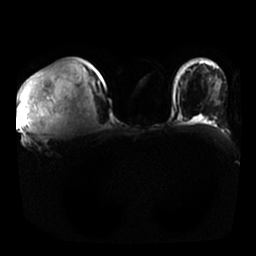
Breast MRI, one axial slice; diffusion-weighted series; image 2 of 4 stored at this slice position (different b-values; order by instance number); 1.5 T; 256 × 256 image matrix. Female patient.
Annotated regions visible in this slice (manually delineated by an expert):
- tumour on diffusion-weighted imaging: bounding box <20,78,41,133> (left, top, right, bottom; pixels)